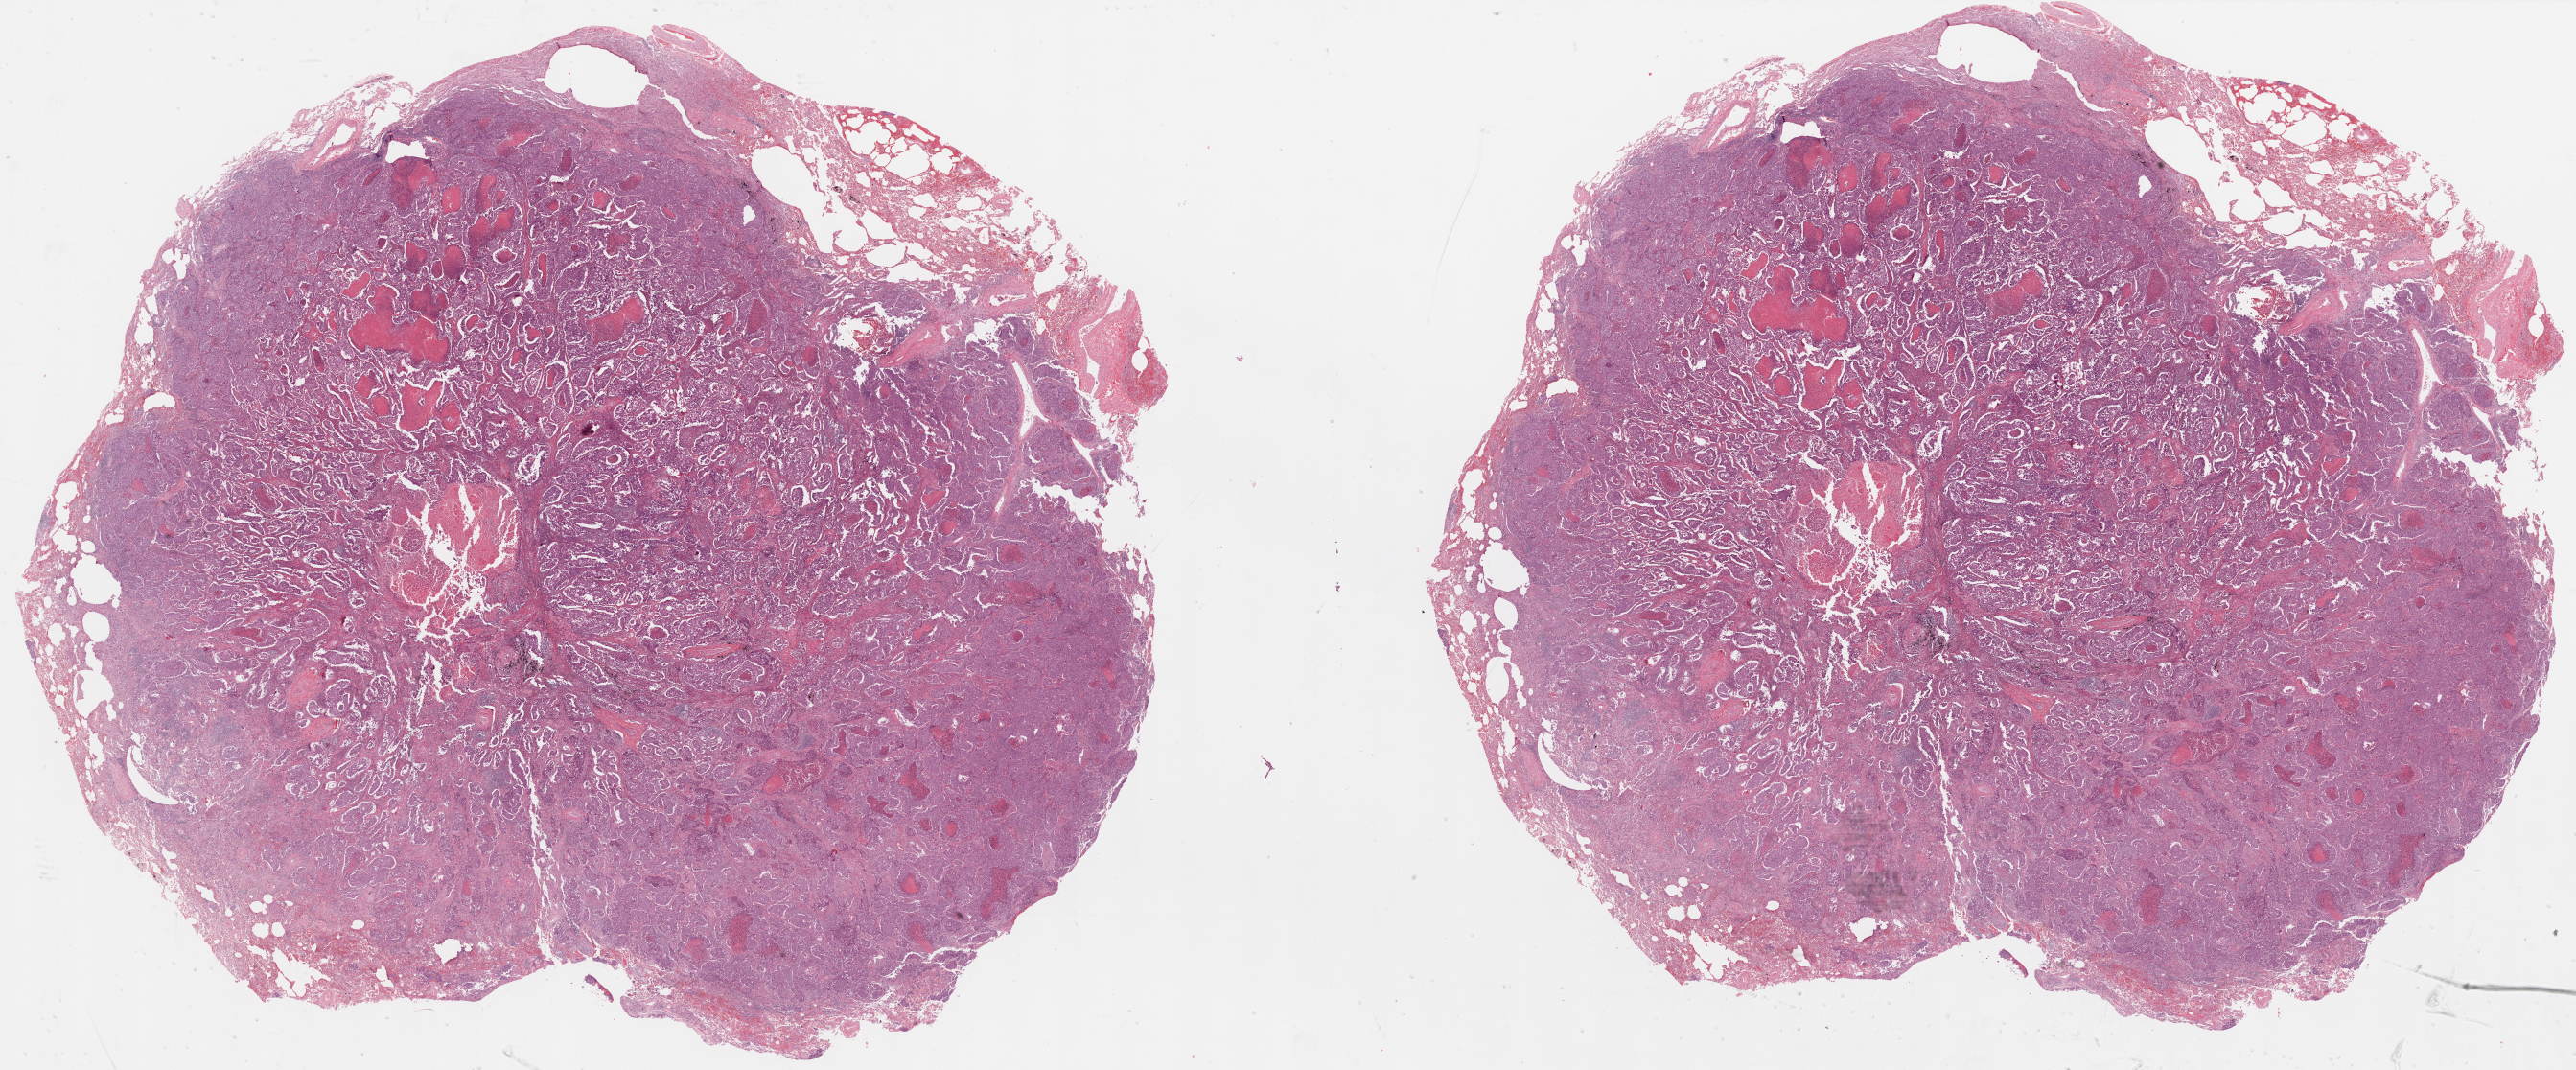
H&E-stained whole-slide image, whole scanned area (about 43.2 x 17.9 mm, from a 20x scan) shown as a low-resolution overview, formalin-fixed paraffin-embedded (FFPE) diagnostic section, primary tumour sample from the lung. Male, age 58 years at initial diagnosis.
Diagnosis: Squamous cell carcinoma, NOS. AJCC pathologic stage: IA.